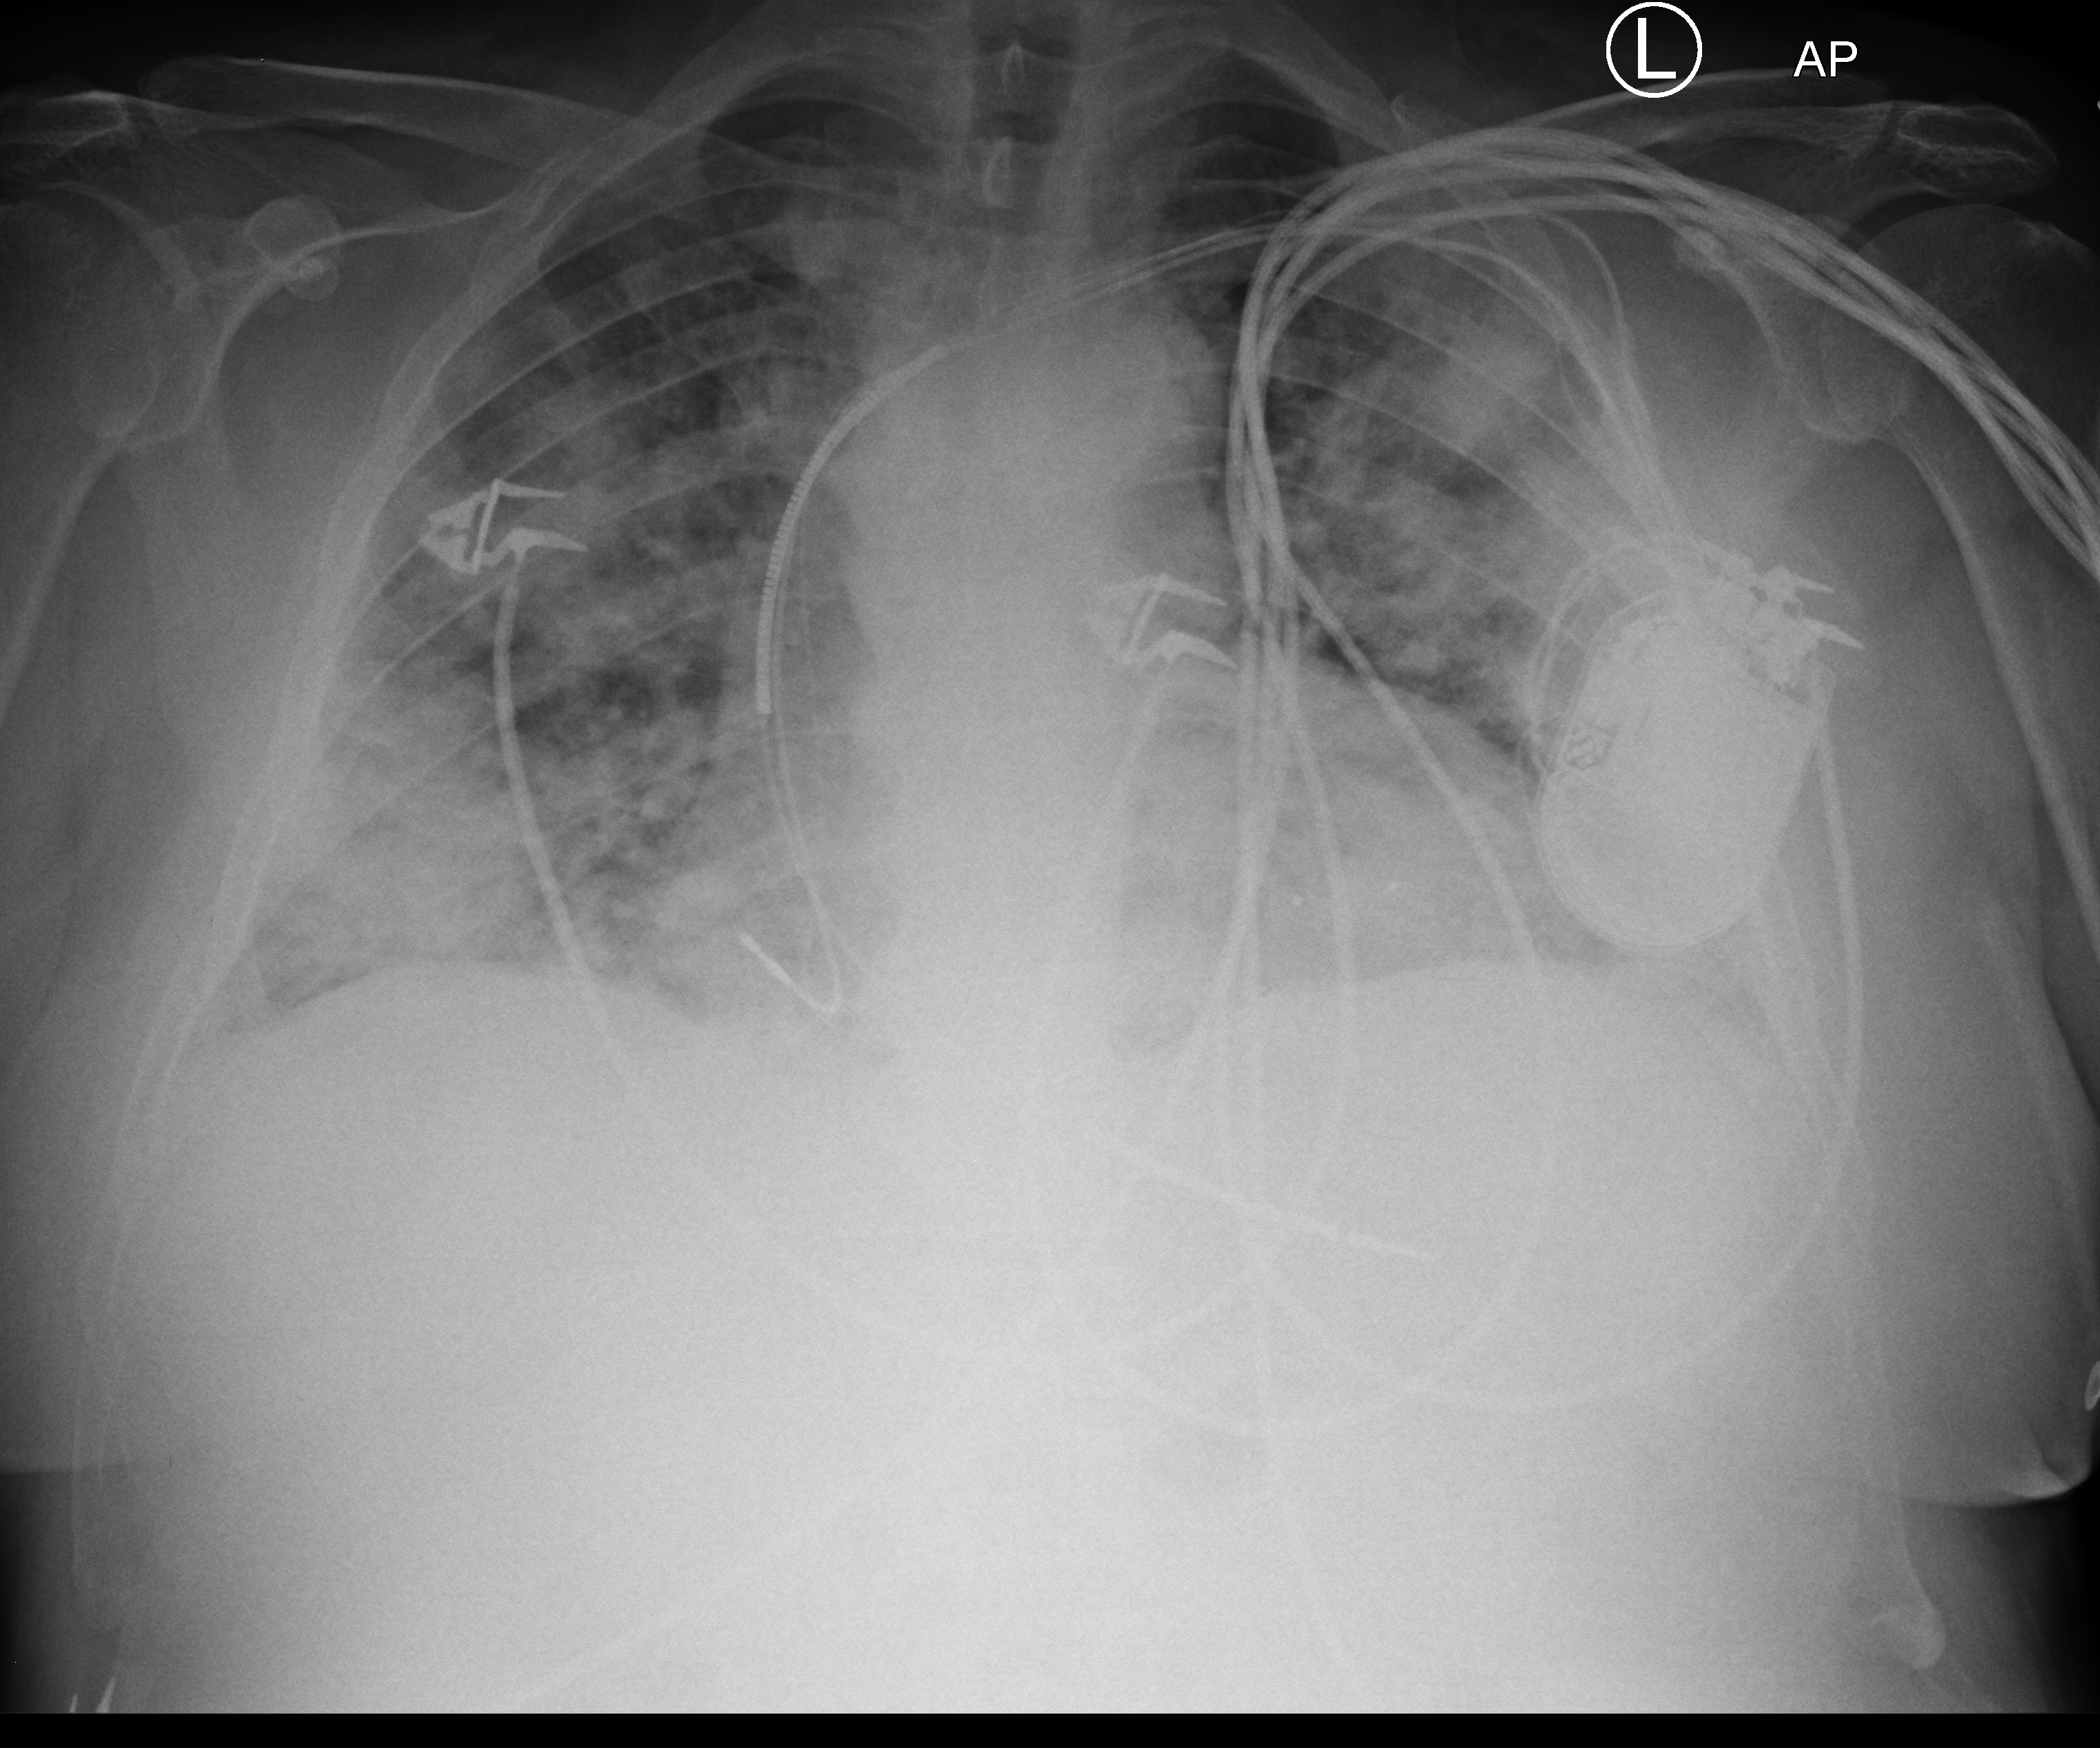
Chest X-ray (portable); anteroposterior (AP) projection. Male patient hospitalised with COVID-19, age 60–74 years.
Admission-level facts for this patient (not findings on this image; timing relative to this image not recorded): hypertension (admission record): yes; smoking status (admission record): former; mechanically ventilated during this hospital stay: no.